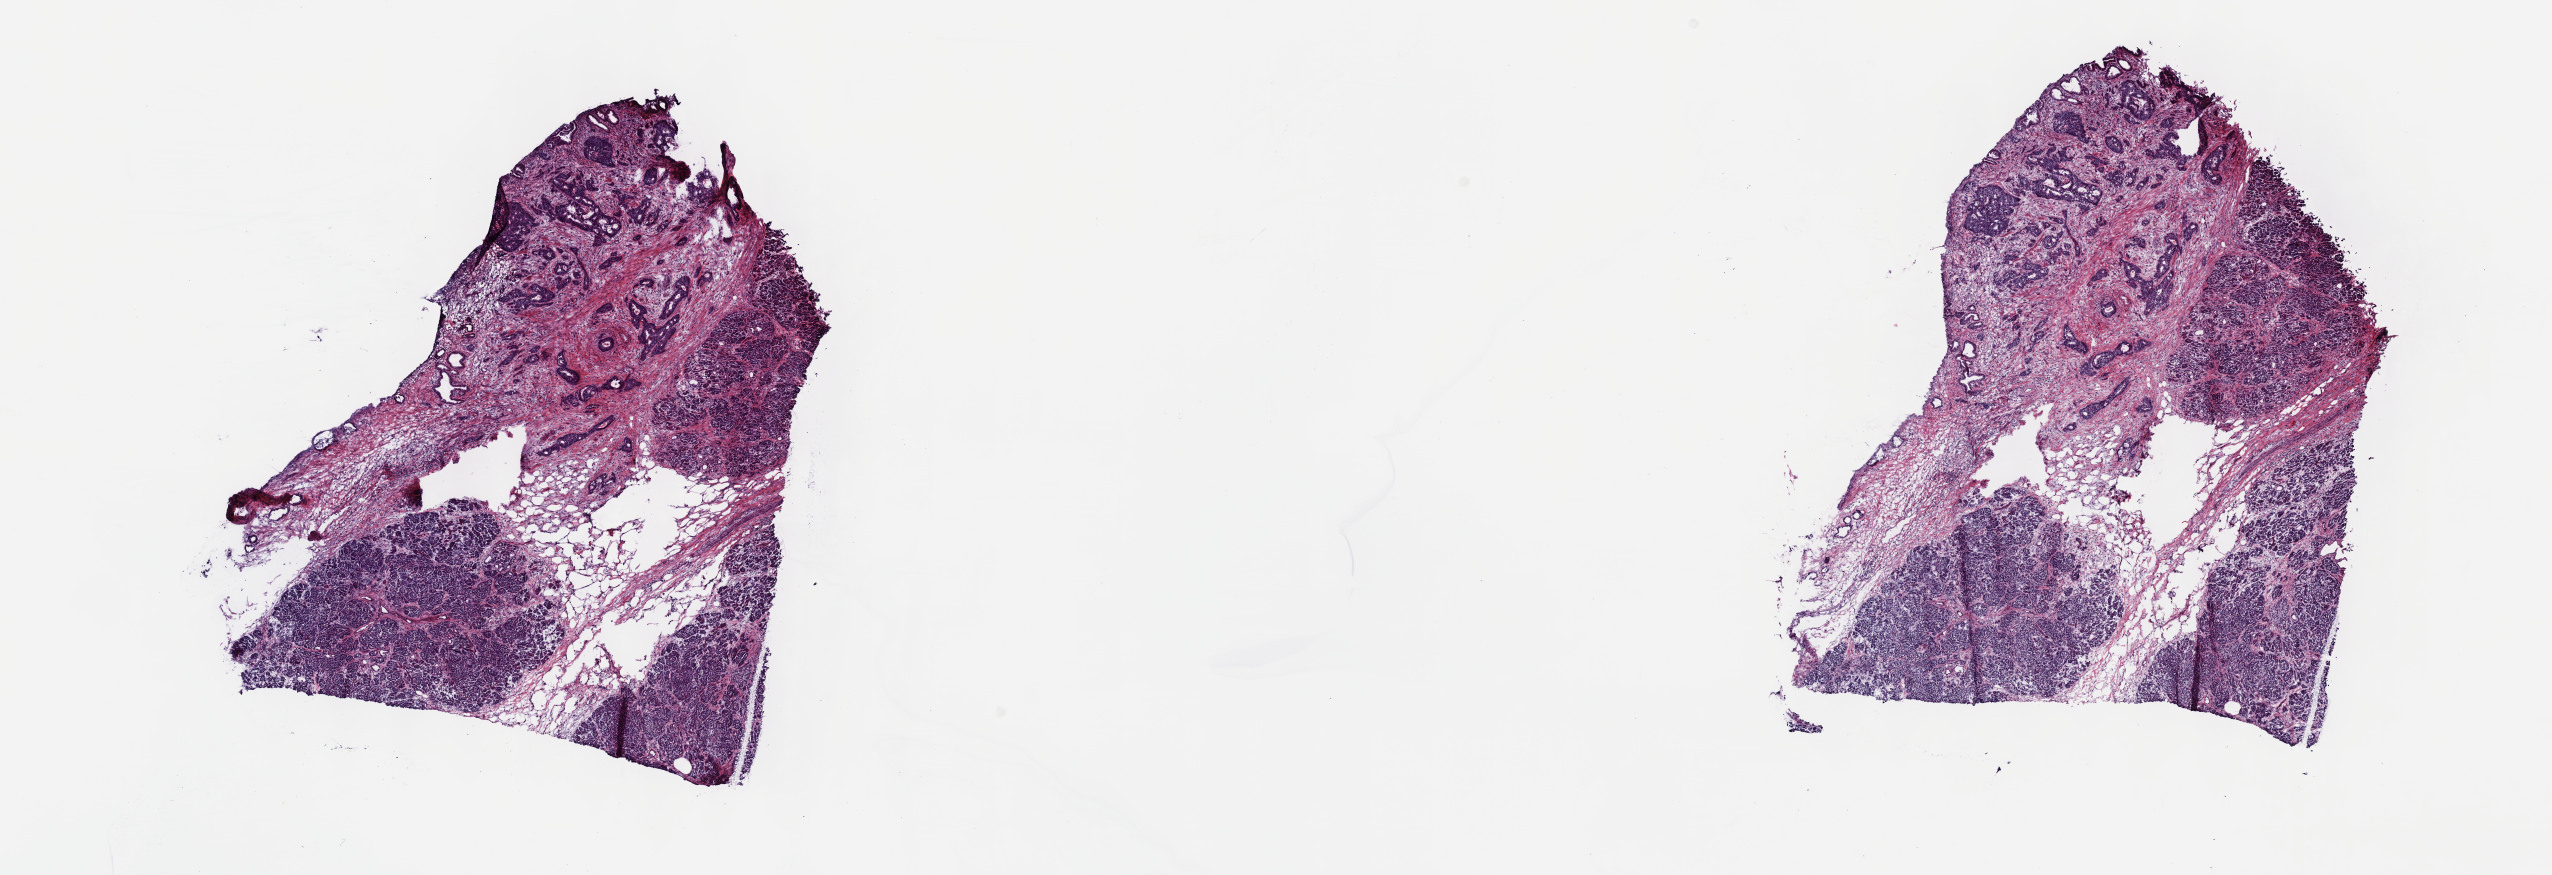
H&E whole-slide image, shown as a low-resolution overview of the whole scanned area (about 20.6 x 7.1 mm, from a 40x scan); frozen section from the top of the tissue portion; primary tumour sample from the pancreas. Patient: male, age at initial diagnosis 74 years. Histologic grade: G4 (undifferentiated). Slide review estimates, as recorded: tumour cells 40%, tumour nuclei 15%, normal cells 60%, stromal cells 0%, necrosis 0%. Infiltration values recorded for this section: lymphocyte infiltration 3%, monocyte infiltration 0%, neutrophil infiltration 0%.
* TNM: T3 N1 M0
* AJCC pathologic stage: IIB
* diagnosis: Infiltrating duct carcinoma, NOS (head of pancreas)